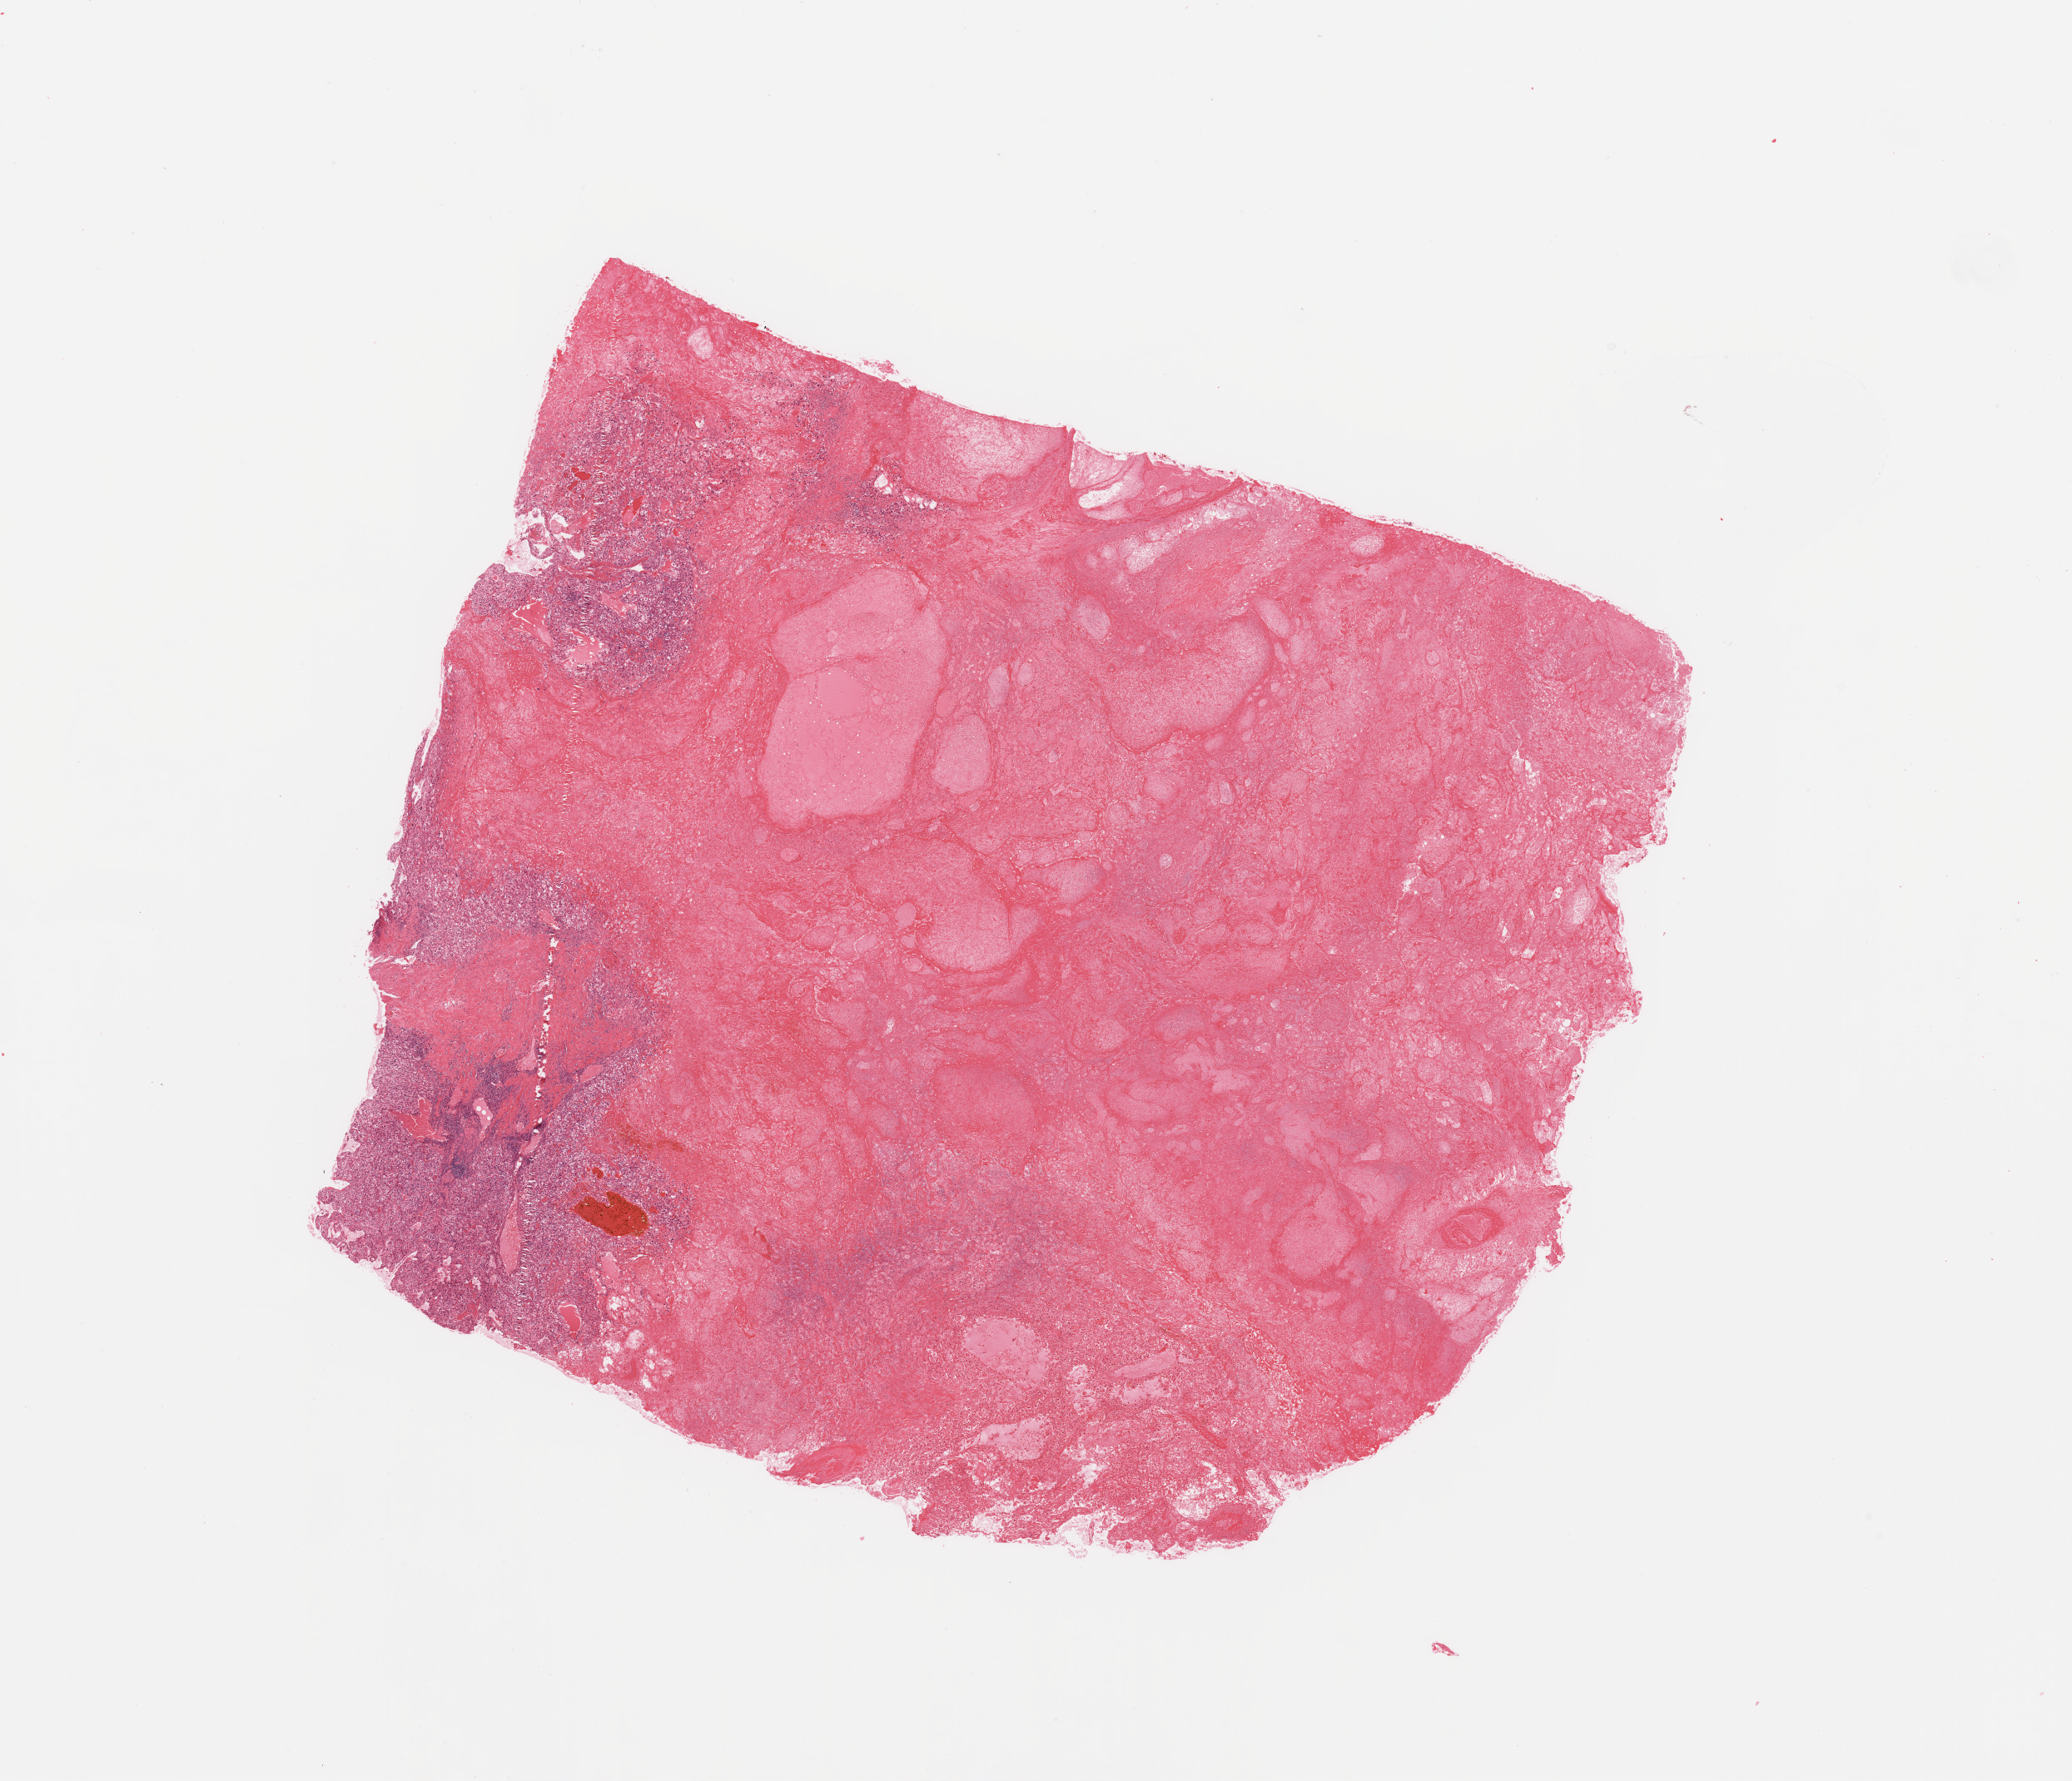
Whole-slide histology image, H&E-stained, a low-resolution overview of the entire scanned area, about 19.7 x 16.9 mm (acquisition: 20x scan); tumour tissue sample, sampled site: kidney. Male, 72 y/o. Histologic grade: G3 (poorly differentiated). Slide review estimates, as recorded: tumour nuclei 50%, necrosis 80%.
AJCC pathologic stage: IV. Diagnosis: Renal cell carcinoma, NOS.